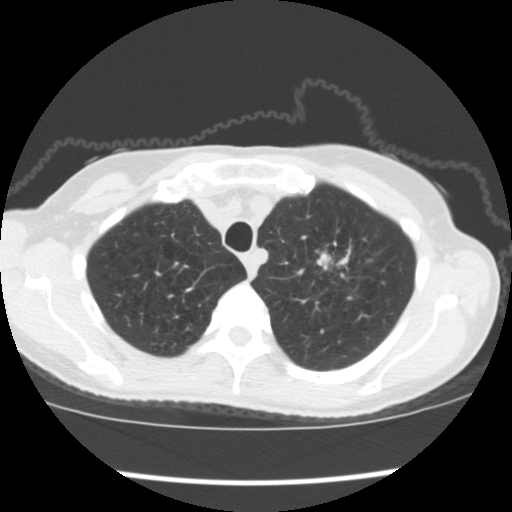
Low-dose screening chest CT, axial slice, baseline annual screen, lung window (W 1500 / L -600 HU), slice 26 of 176 in the series. Female, age 67 years at enrolment. Former smoker at enrolment.
Lesion marked by an expert reader, bounding box [x1, y1, x2, y2] px = [302, 235, 375, 310]. Reader record for this screening exam (exam-level; its link to the box is not recorded): non-calcified nodule or mass ≥4 mm, left upper lobe, 34 × 32 mm, spiculated (stellate) margins, soft tissue attenuation, pre-existing on the prior screen: no. Participant outcome: lung cancer diagnosed 17 days after this screen — small cell carcinoma, NOS, left upper lobe, stage IIIA (AJCC 6th edition), 40 mm at pathology.